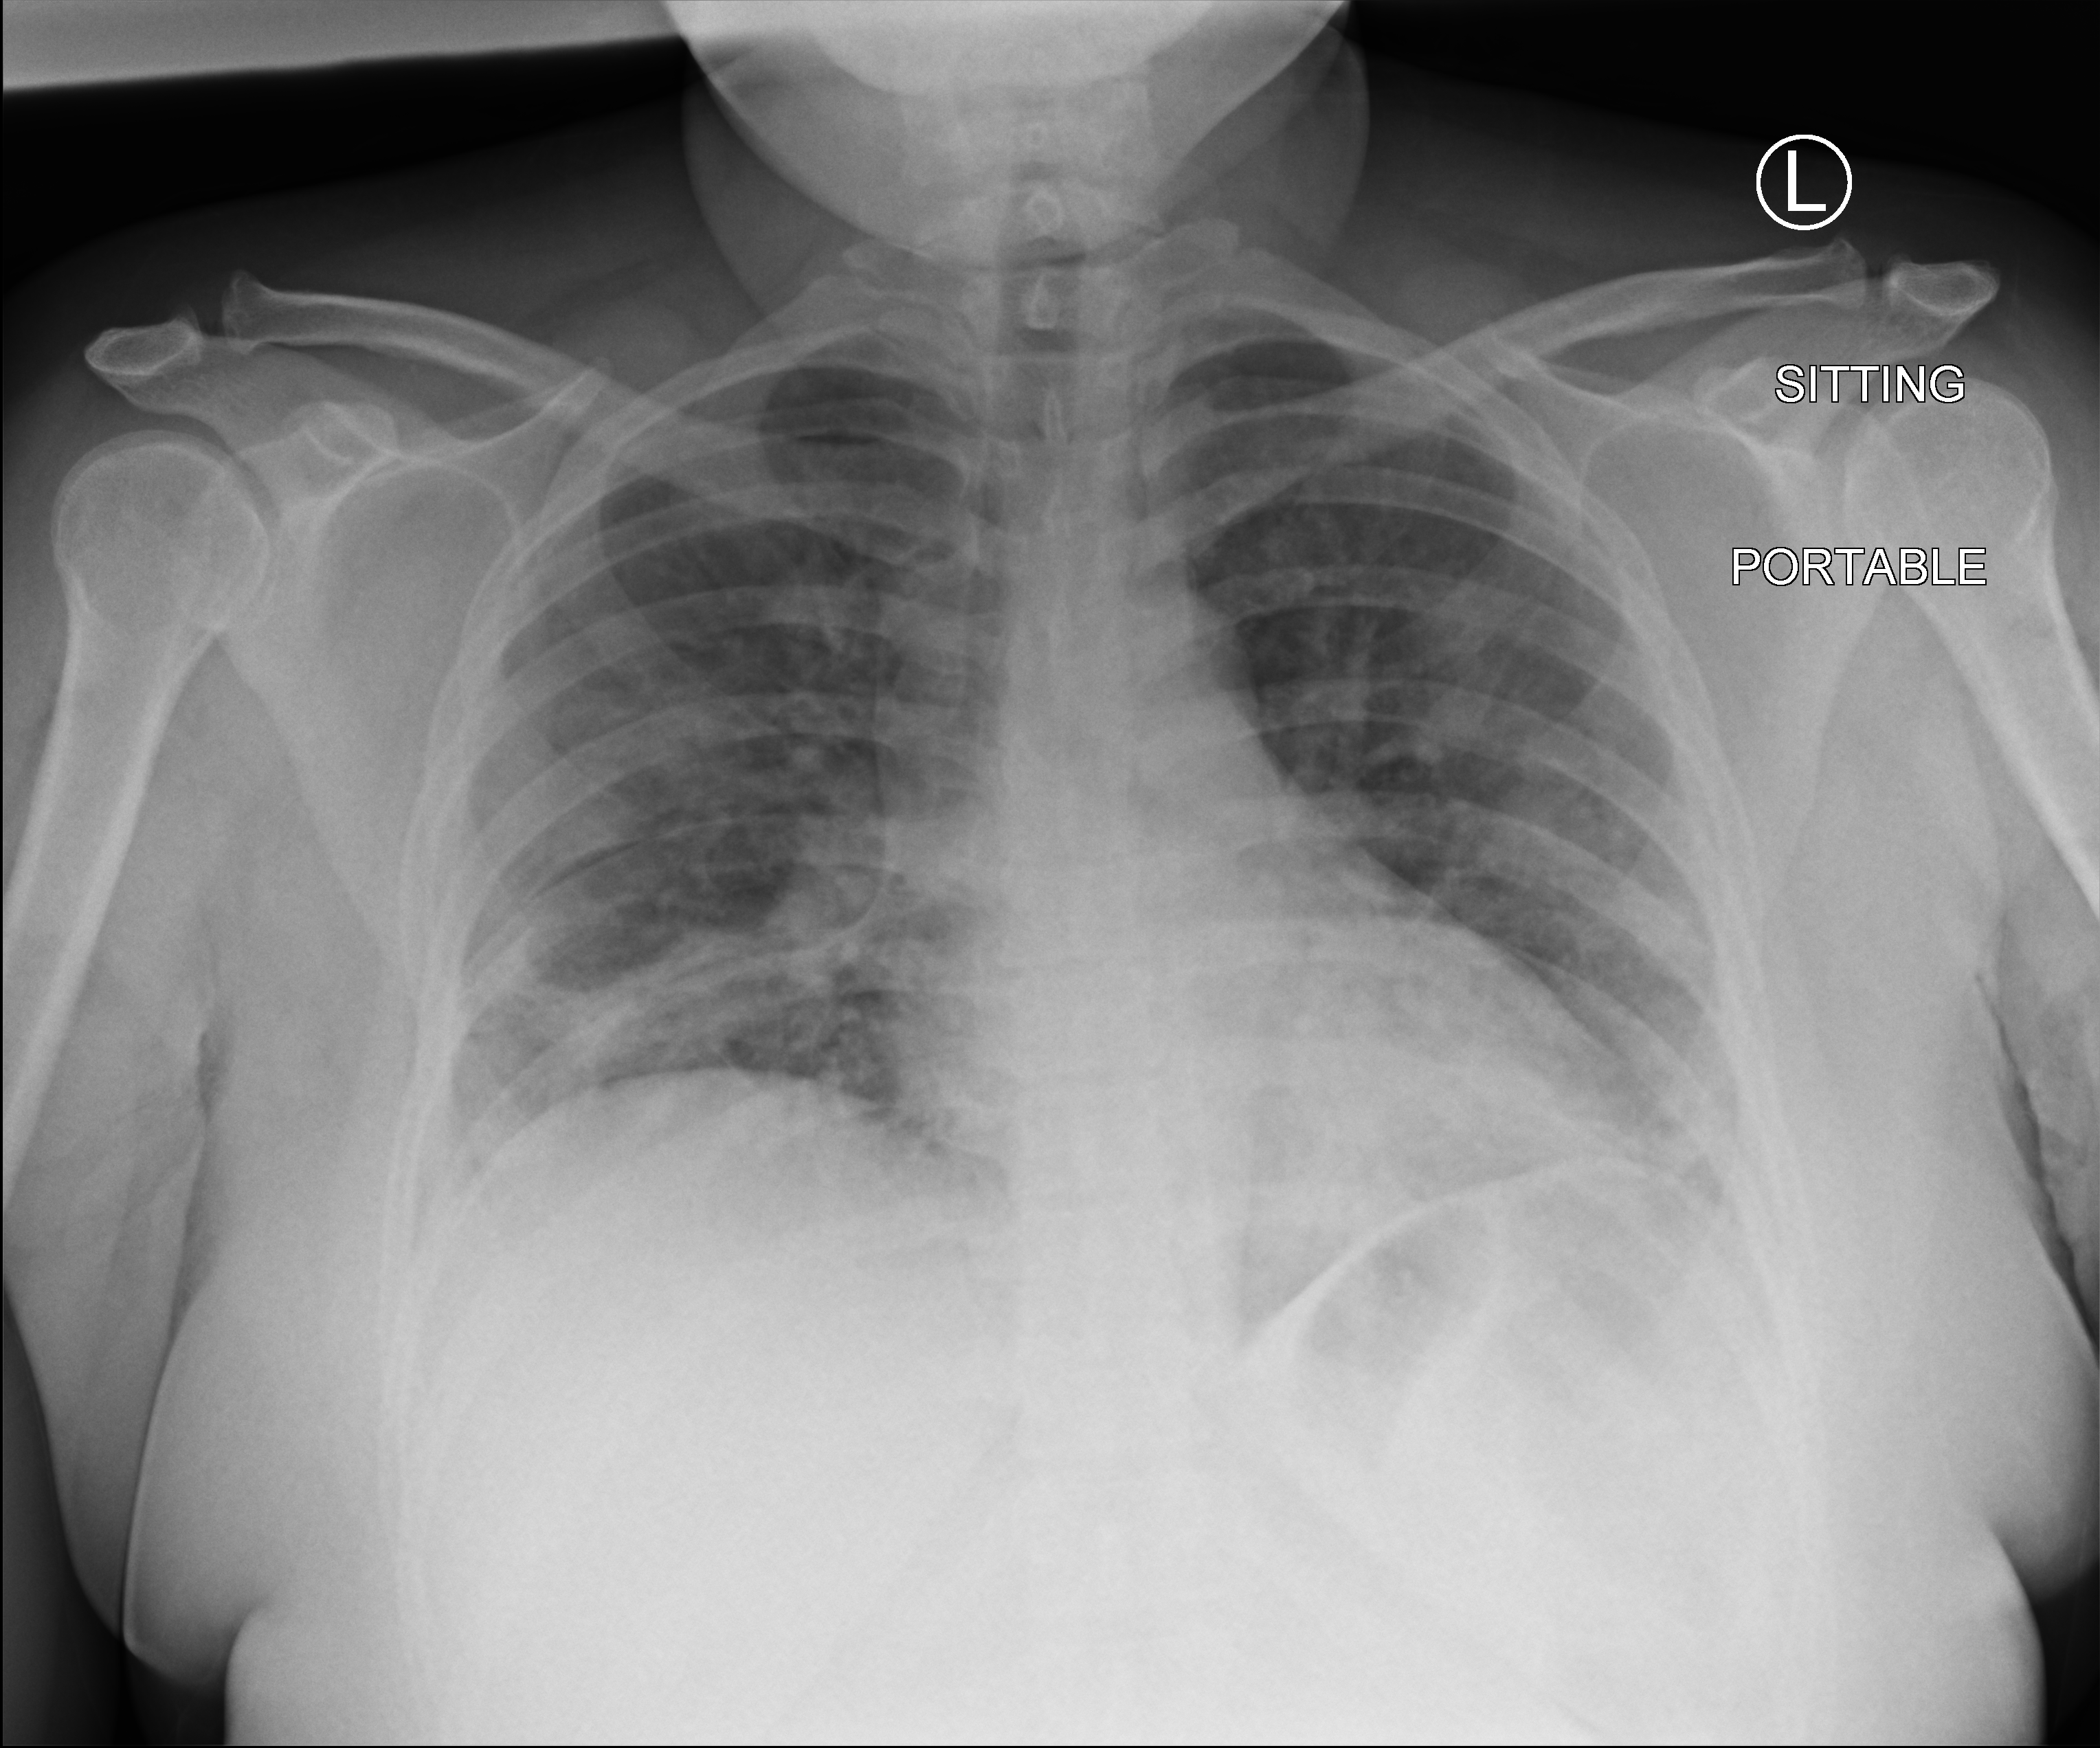
Bedside chest radiograph (computed radiography). Patient hospitalised with COVID-19; female, aged 18–59 years.
Admission-level facts for this patient (not findings on this image; timing relative to this image not recorded): length of hospital stay: 16 days; mechanically ventilated during this hospital stay: yes; admitted to intensive care during this hospital stay: no.